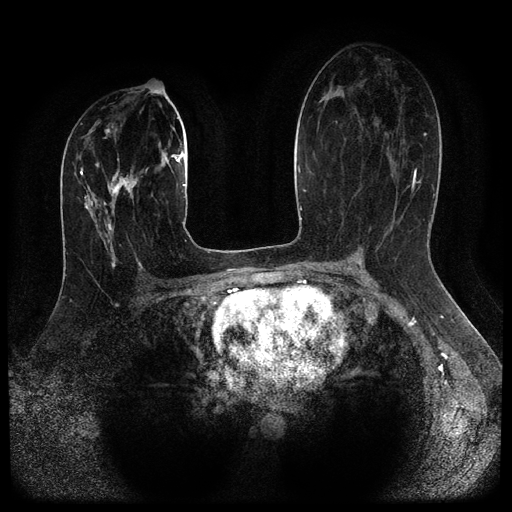
Breast MRI (dynamic contrast-enhanced, multi-phase), one axial slice. Dynamic contrast-enhanced series, time point 2 of 5 at this slice position (early post-contrast). 1.5 T. TE 2.6 ms, TR 5.4 ms. 2 mm slice thickness. 512 × 512 image matrix, field of view 340 × 340 mm. Female patient, age 29 years.
Annotated regions visible in this slice (semi-automatic segmentation, software-assisted and operator-edited):
- breast lesion (labelled 'tumour' in the annotation; benign lesions carry a separate 'benign' label): bounding box (x1, y1, x2, y2) in pixels: (105, 168, 138, 206)